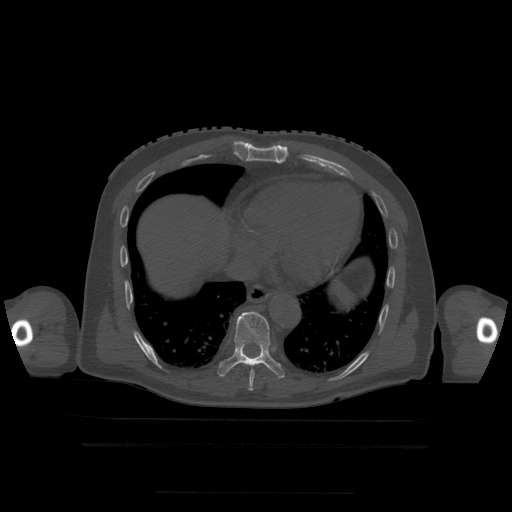
CT including the spine, one axial slice. Slice 264 of 522 in the series (ordered by position). Bone window (W 1800 / L 400 HU). 512 × 512 image matrix, field of view 436 × 436 mm. Patient age 68 years. Case-level facts recorded for this patient, not image findings: primary cancer: urothelial.
Annotated regions visible in this slice (semi-automatically segmented with operator editing):
- T7 vertebra: box from (x=248, y=384) to (x=254, y=393) px
- T8 vertebra: (x=250, y=371)–(x=255, y=384)
- T9 vertebra: (x=217, y=312)–(x=285, y=379)